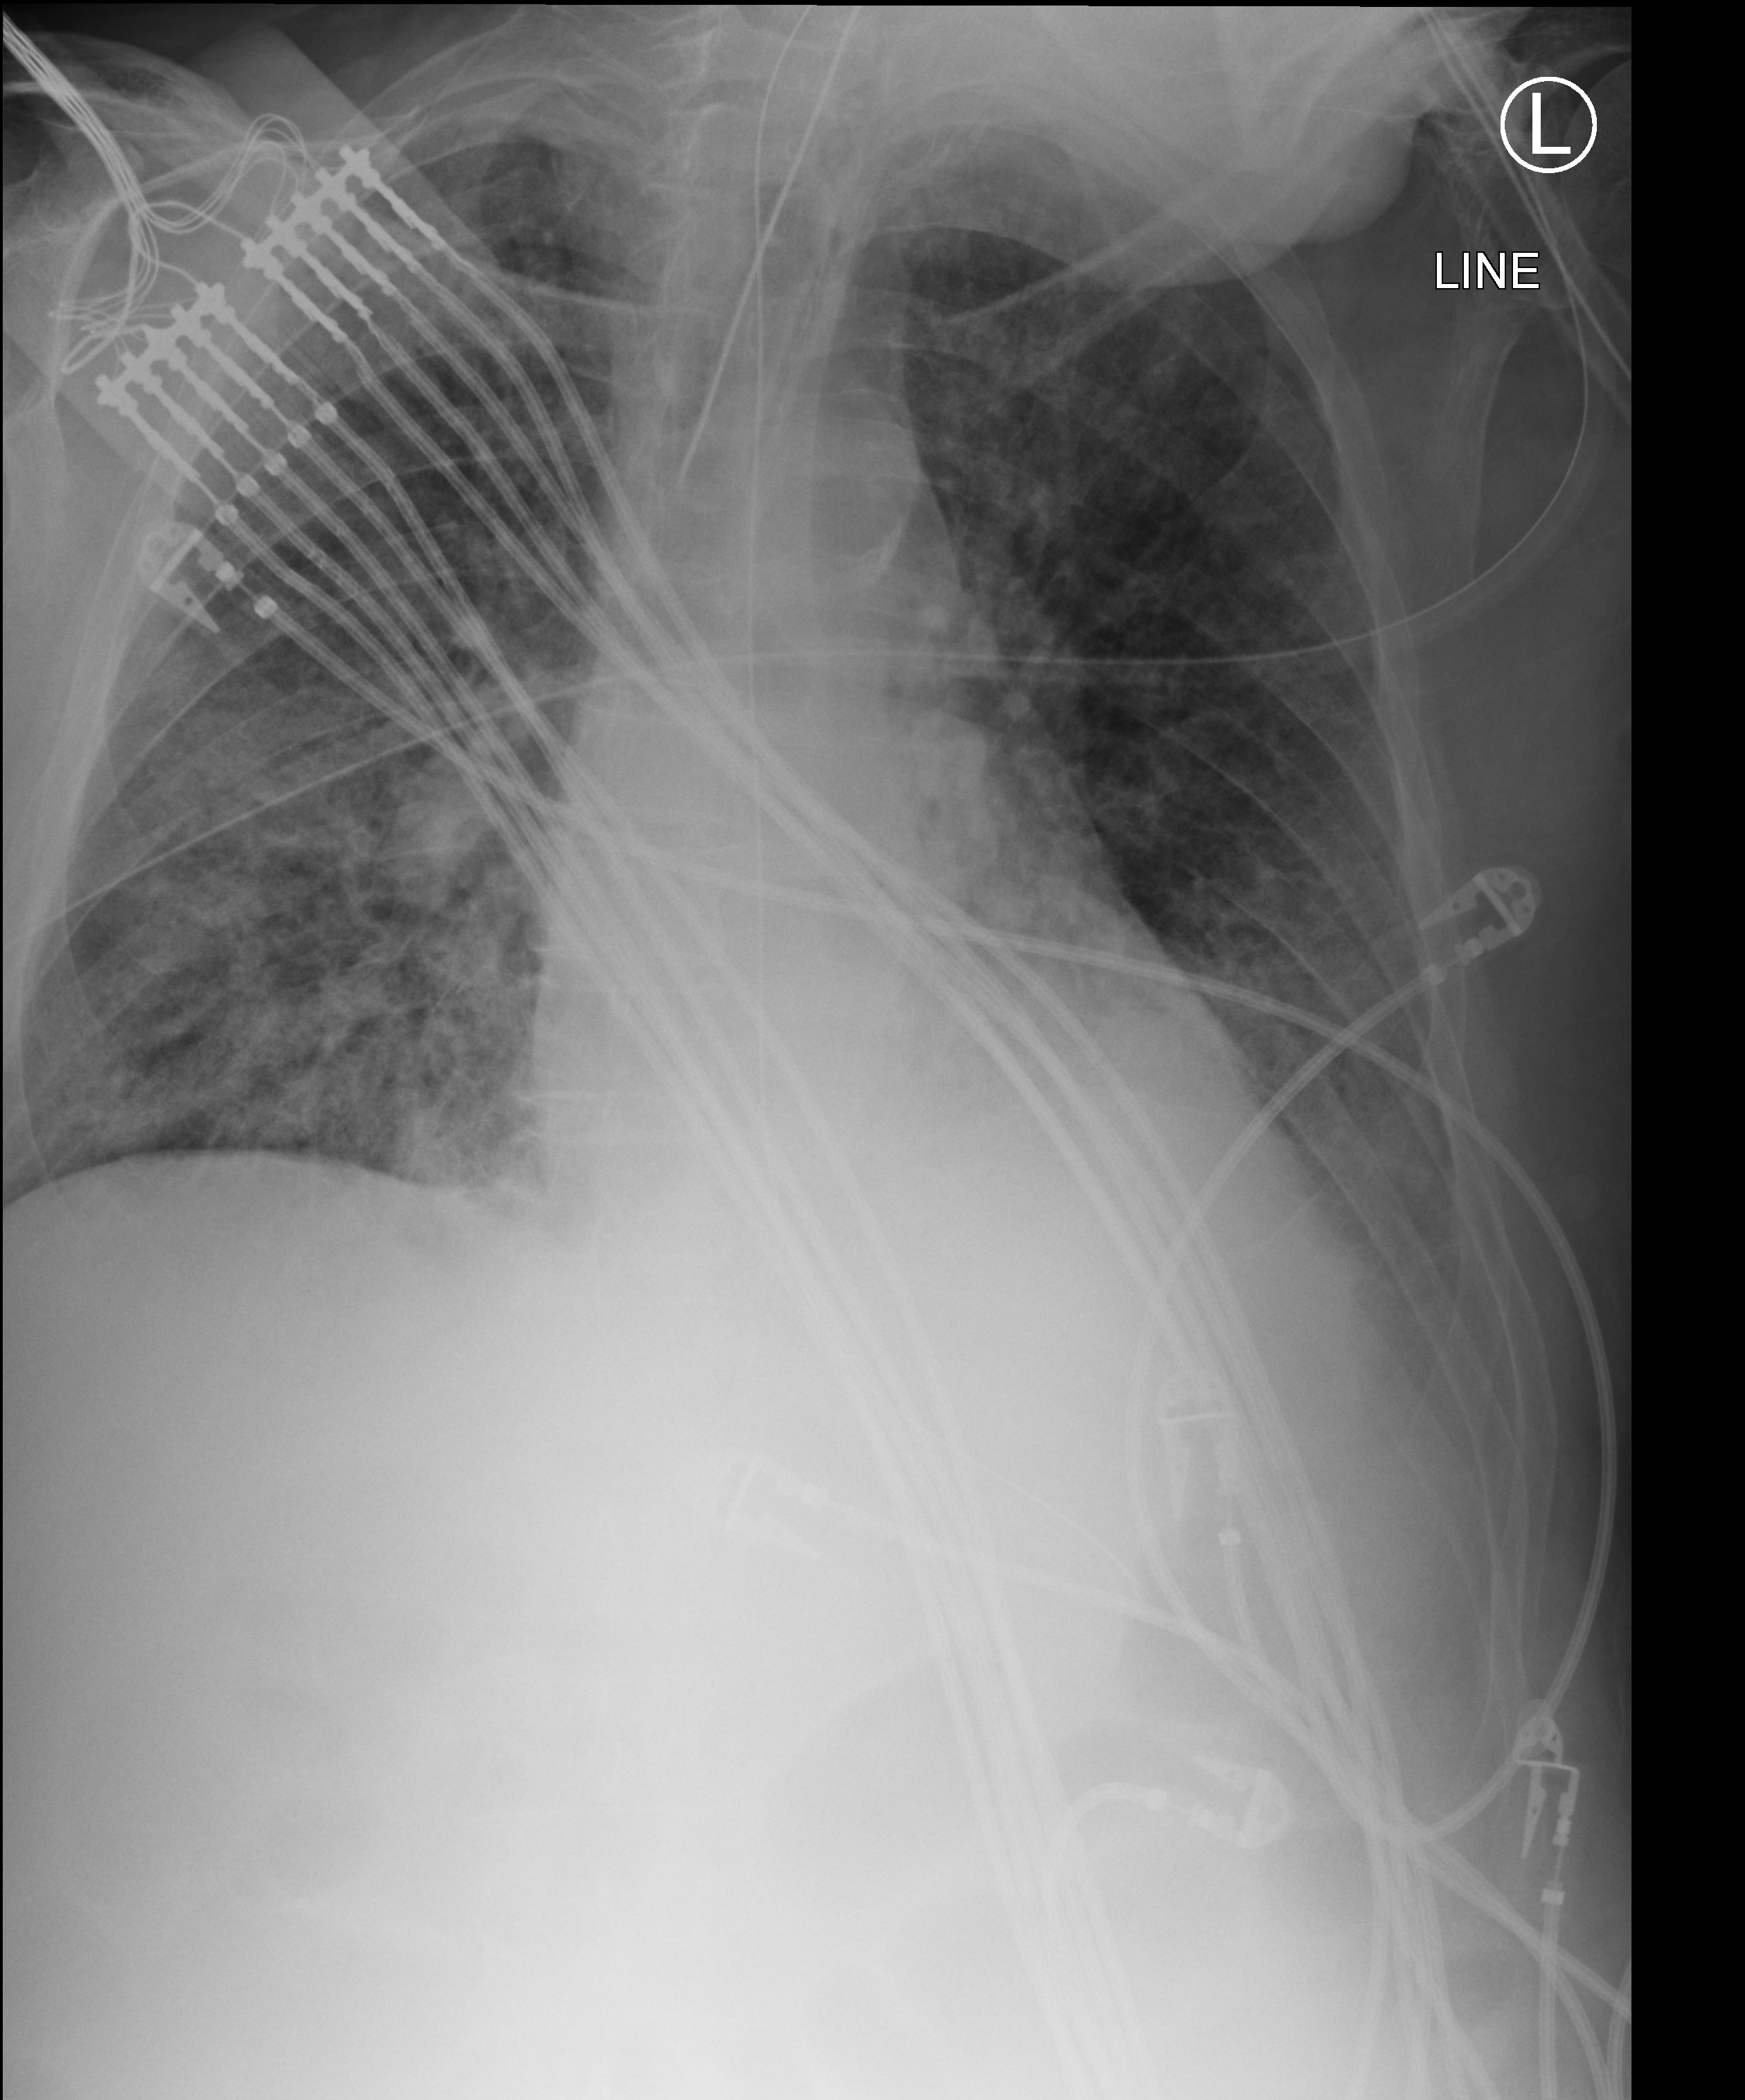
Portable chest radiograph; anteroposterior (AP) projection. Patient hospitalised with COVID-19; male, aged 60–74 years.
Admission-level facts for this patient (not findings on this image; timing relative to this image not recorded): admitted to intensive care during this hospital stay: yes; diabetes (admission record): no.